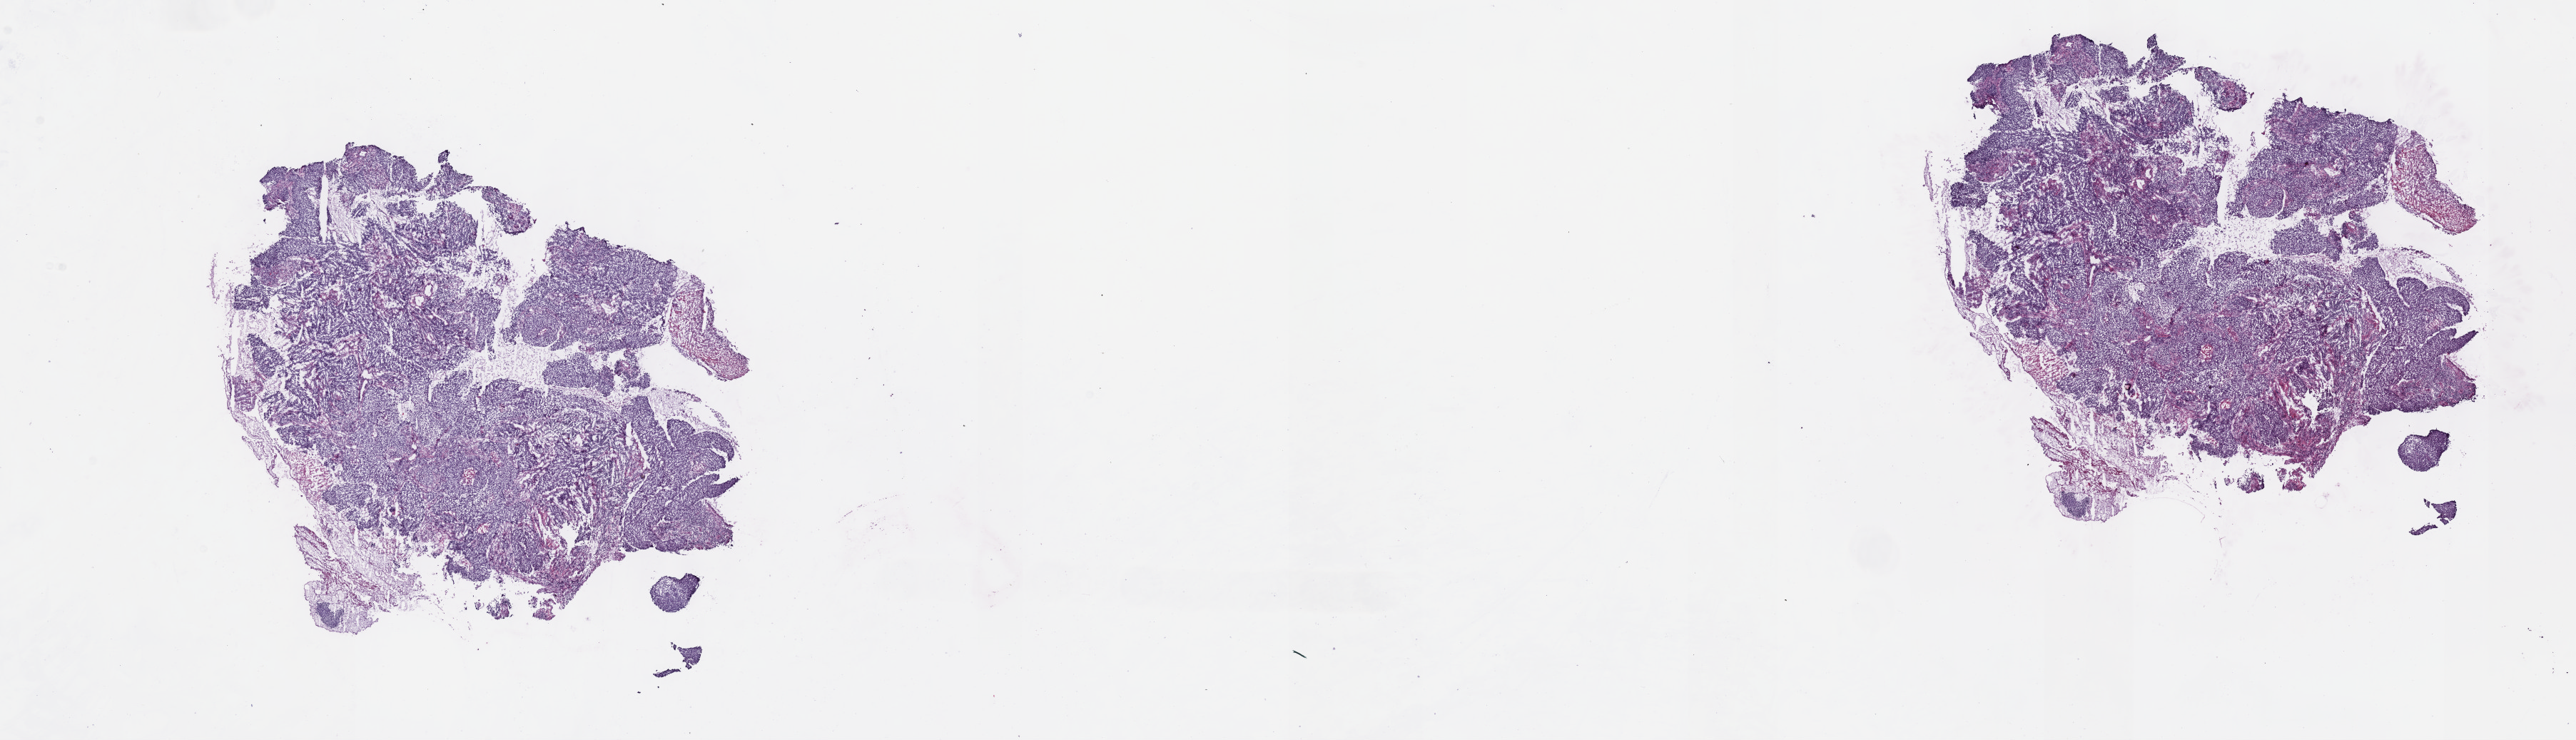
Whole-slide histology image, H&E-stained, a low-resolution overview of the entire scanned area, about 29.2 x 8.4 mm (slide scanned at 40x); frozen section; cervix, primary tumour sample. Female patient; age at initial diagnosis 73 years. Composition of this section per pathologist review: tumour cells 80%, tumour nuclei 80%, normal cells 5%, stromal cells 10%, necrosis 5%. Infiltration values recorded for this section: lymphocyte infiltration 5%, monocyte infiltration 0%, neutrophil infiltration 0%.
Pathologic diagnosis: Squamous cell carcinoma, large cell, nonkeratinizing, NOS (cervix uteri).